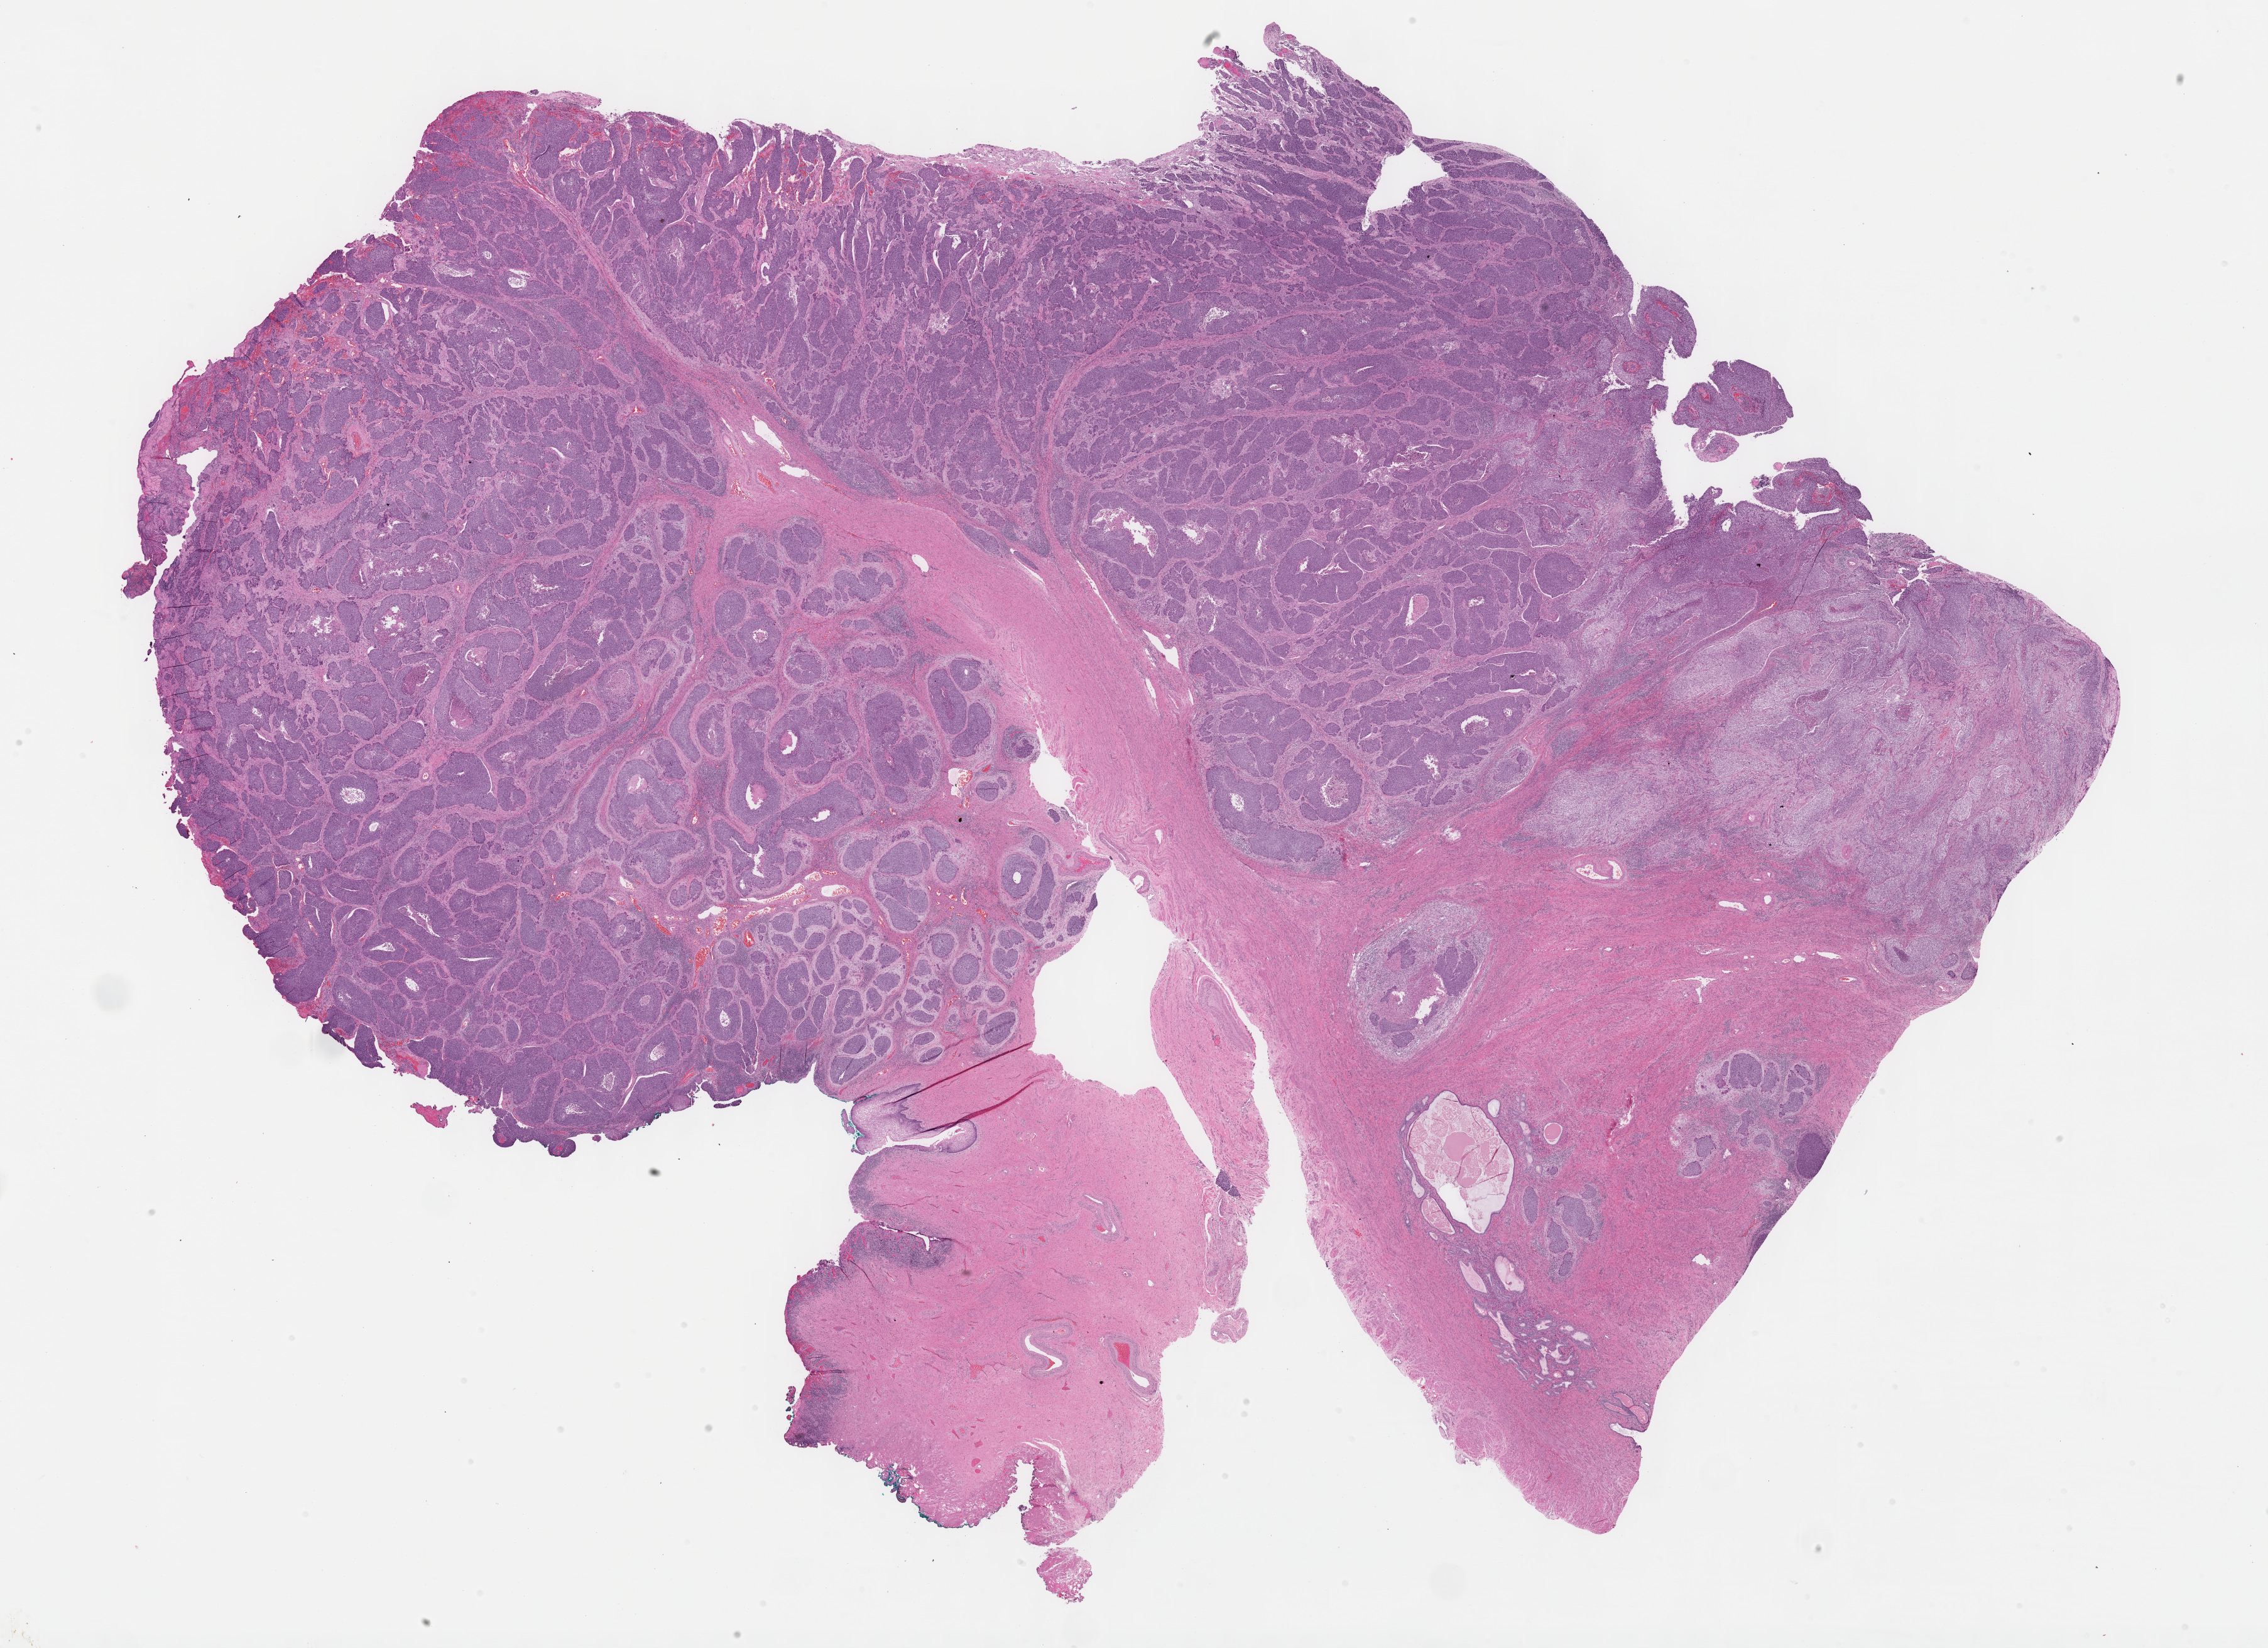
Whole-slide histology image, H&E — low-resolution overview of the scanned area, about 29.2 x 21.2 mm, formalin-fixed paraffin-embedded (FFPE) diagnostic section, primary tumour sample from the cervix. Patient: female, age at initial diagnosis 57 years. Histologic grade: G3 (poorly differentiated).
Histologic diagnosis: Squamous cell carcinoma, NOS (cervix uteri). Lymph nodes positive (case pathology): 4 of 28 examined.